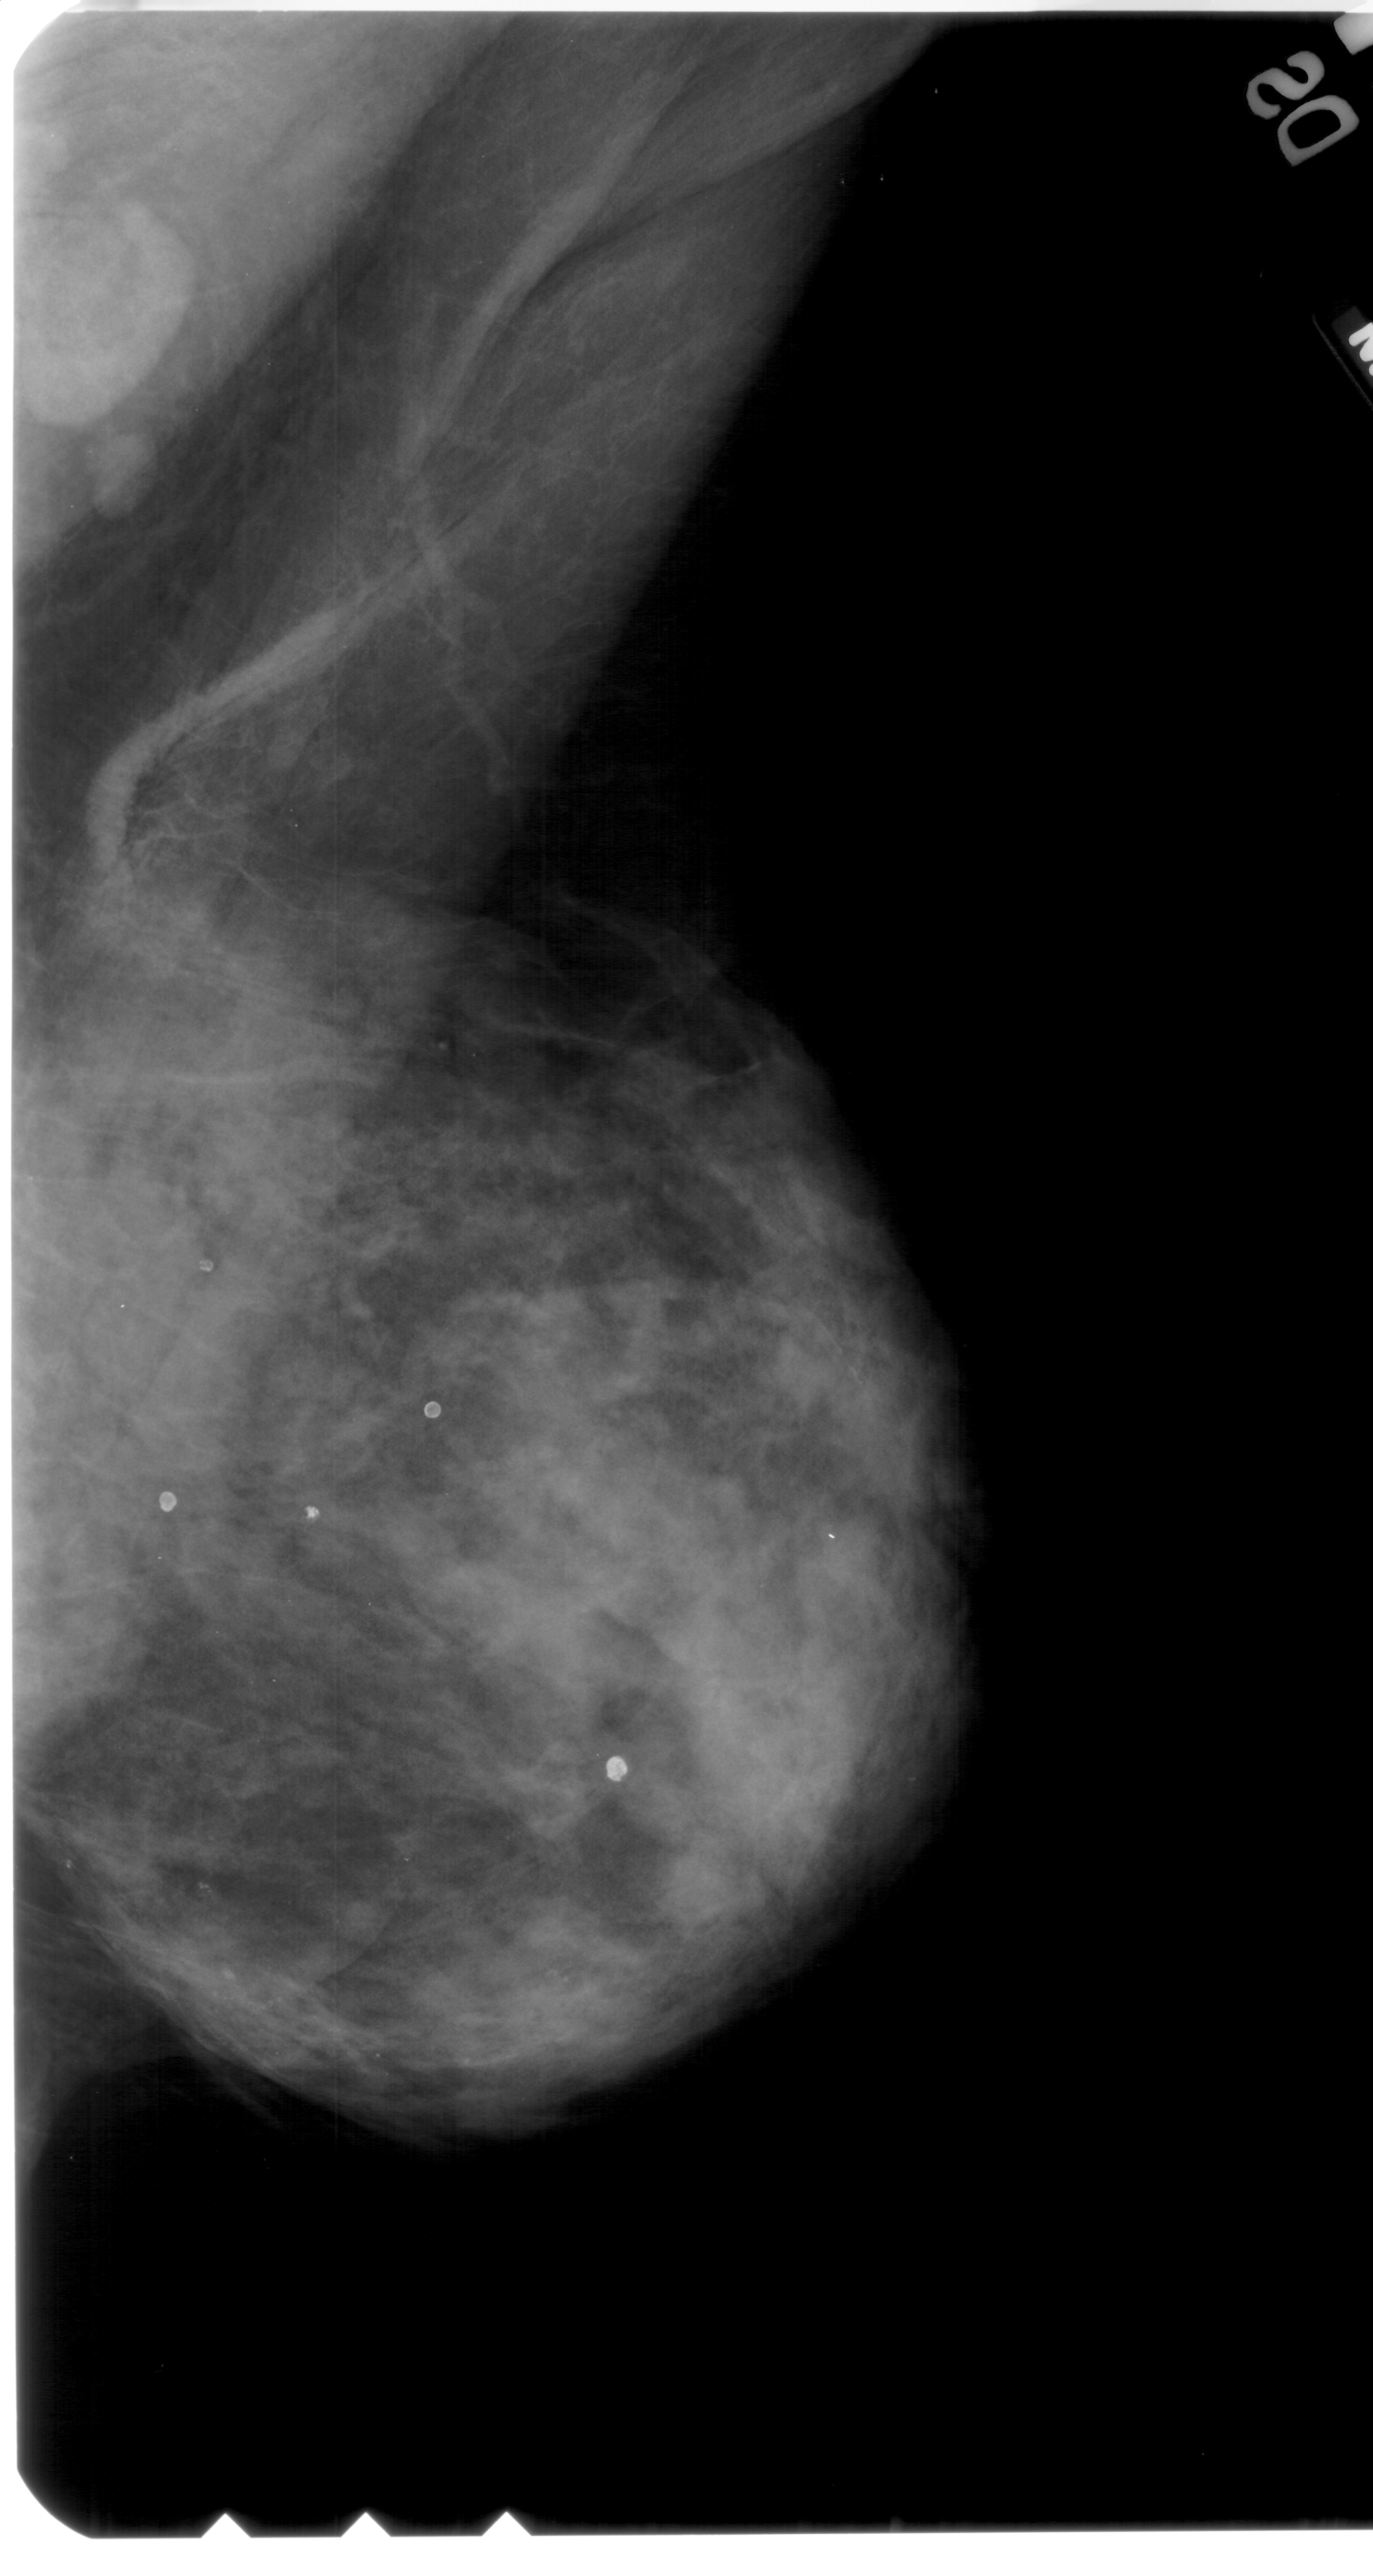
Mammogram (digitized film); right breast; MLO view; breast composition: extremely dense (BI-RADS density category 4 of 4); 1373 × 2576 image matrix.
Expert-marked regions of interest on this film, with their recorded descriptors:
- calcifications, morphology pleomorphic, distribution clustered; BI-RADS assessment category 4; pathology (as recorded): benign: bounding box [x1, y1, x2, y2] px = [185, 1870, 371, 2071]